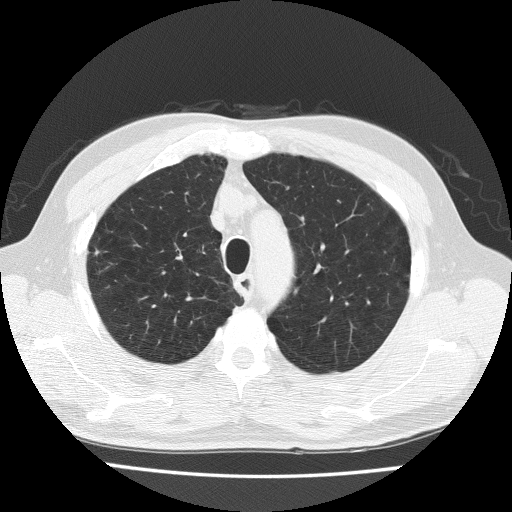
Chest CT (low-dose screening protocol), one axial image; first (baseline) screen; lung window (W 1500 / L -600 HU); 512 × 512 image matrix, field of view 350 × 350 mm. Male, age 73 years at enrolment.
Expert-annotated lung lesion, bounding box (x1, y1, x2, y2) in pixels: (83, 238, 113, 267). Screening reader's record for this exam (one nodule recorded; not confirmed to be the boxed lesion): non-calcified nodule or mass ≥4 mm, right upper lobe, 4 × 4 mm, spiculated (stellate) margins, soft tissue attenuation. Official screen result: positive, change unspecified: nodule(s) >= 4 mm or enlarging nodule(s), mass(es), or other non-specific abnormalities suspicious for lung cancer. Later outcome: lung cancer diagnosed 170 days after this screen — adenocarcinoma, NOS, right upper lobe, poorly differentiated (G3), stage IA (AJCC 6th edition), 60 mm at pathology.